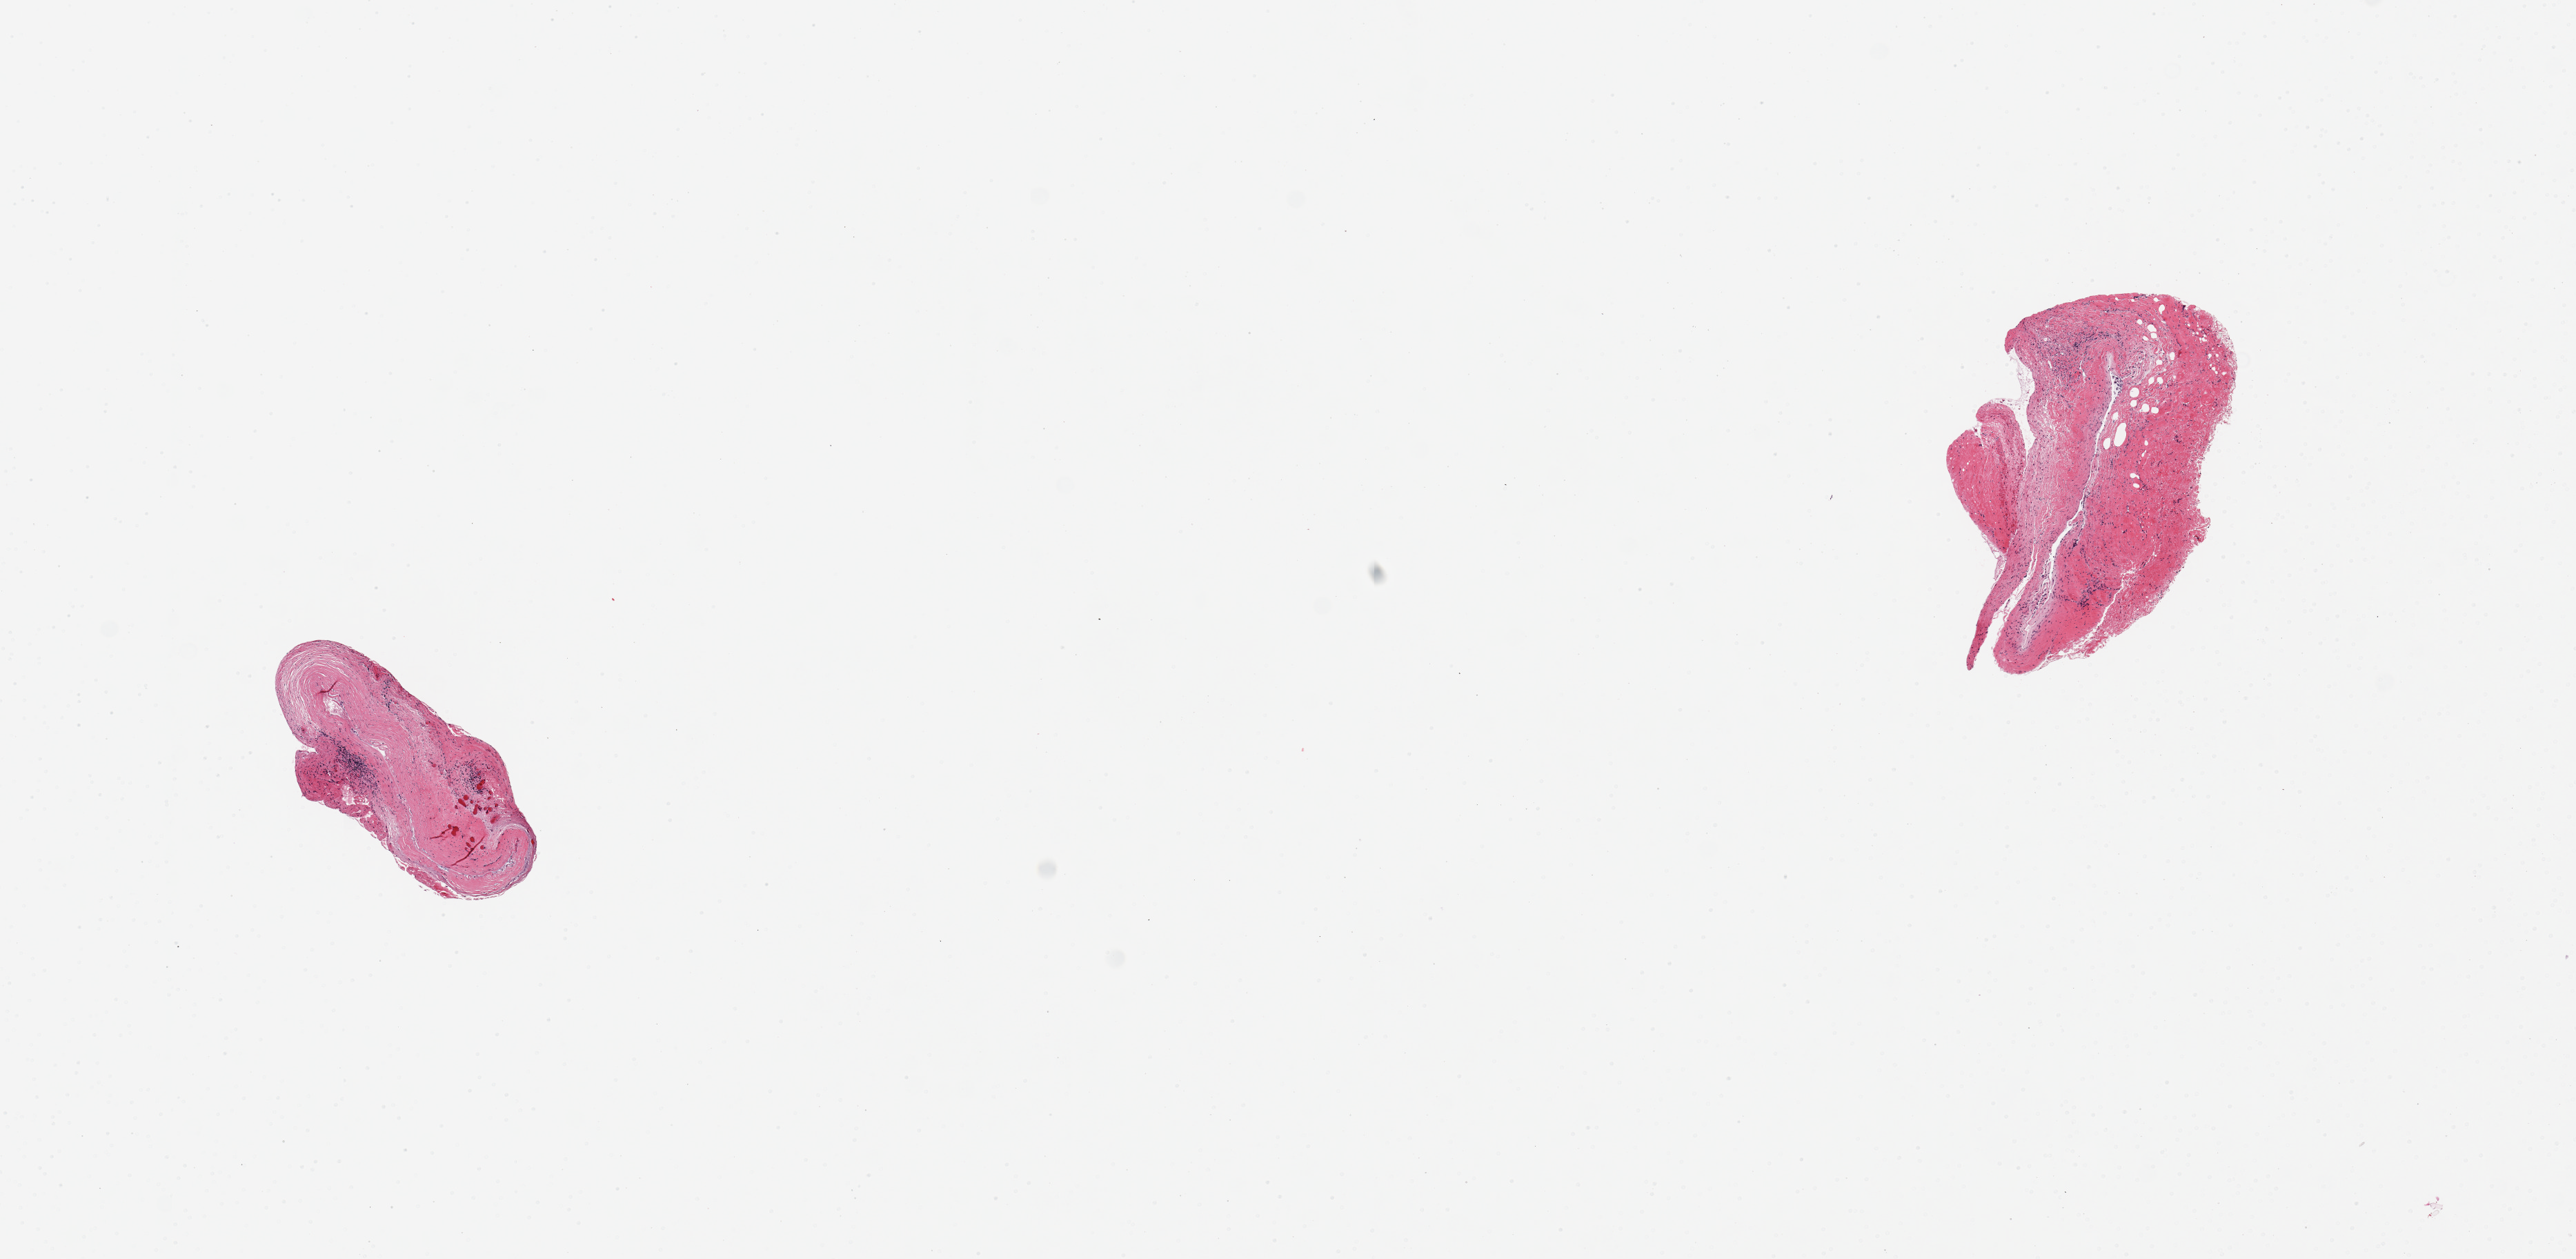
Digitized H&E-stained section — a low-resolution overview of the entire scanned area, about 14.8 x 7.2 mm (acquisition: 20x scan). PAXgene-fixed paraffin-embedded (PFPE) section. Target tissue: coronary artery. Tissue donor sample. Female donor.
Pathologist's review note for this sample: 2 pieces, subtotally occlusive atherosis.